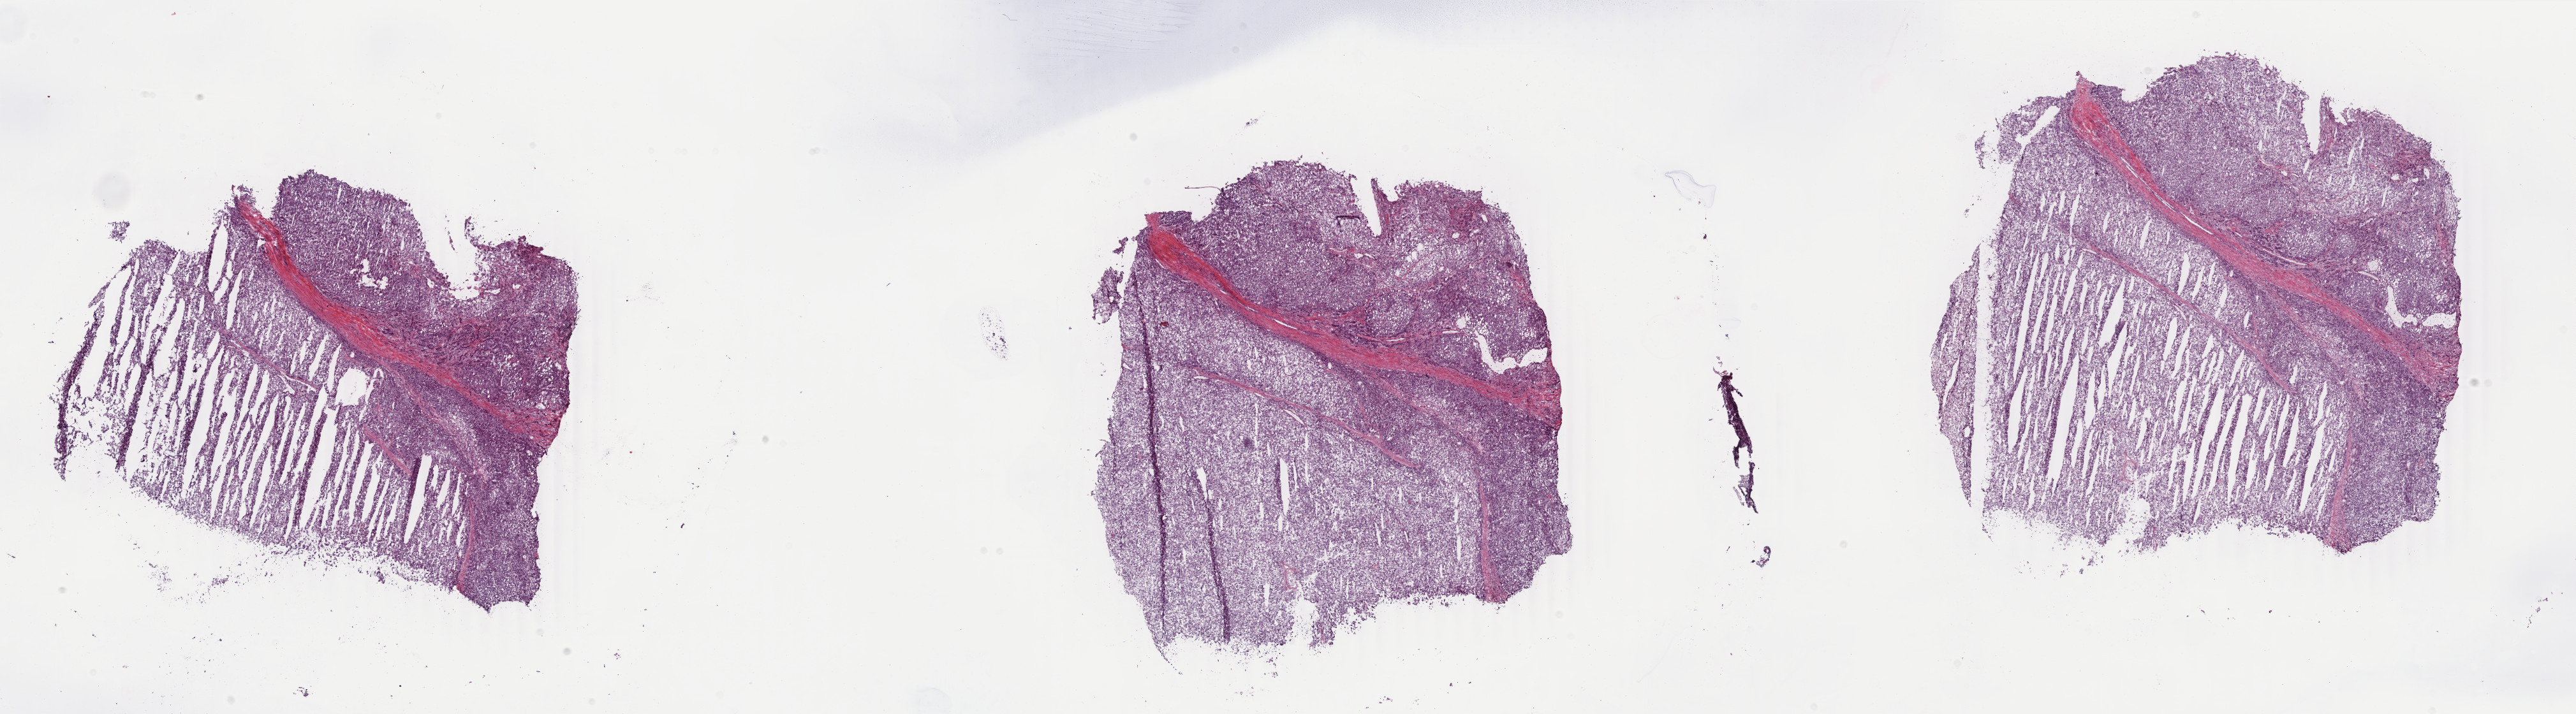
Digitized Hematoxylin and eosin (H&E) stained tissue section (whole slide), shown as a low-resolution overview of the whole scanned area (about 32.1 x 8.9 mm, slide scanned at 40x). Frozen section from the top of the tissue portion. Primary tumour sample from the liver. Male patient; age at initial diagnosis 61 years. Histologic grade: G1 (well differentiated). Pathologist review of this section (percent, as recorded): tumour cells 90%, tumour nuclei 80%, normal cells 0%, stromal cells 10%, necrosis 0%. Infiltration values recorded for this section: lymphocyte infiltration 3%, monocyte infiltration 0%, neutrophil infiltration 0%.
AJCC pathologic stage: IIIA (6th edition). Diagnosis: Hepatocellular carcinoma, NOS.